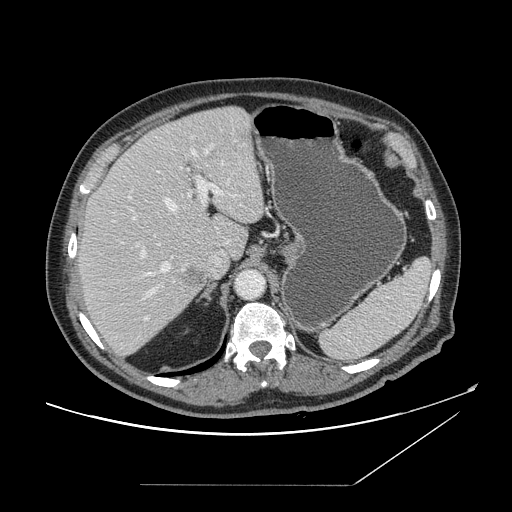
Contrast-enhanced abdominal CT, one axial slice. Position 110 of 166 along the scan axis. Intravenous contrast given. Soft-tissue window (W 400 / L 40 HU). 2.5 mm slice thickness. 512 × 512 image matrix. Male patient, age 80 years. Case-level facts recorded for this patient, not image findings: diagnosis: colorectal cancer liver metastases, imaged before liver resection; multiple liver metastases: no; largest metastasis: 2.2 cm; disease in both lobes: no.
Outlined on this slice (expert manual segmentation):
- hepatic veins: bounding box <133,150,196,298> (left, top, right, bottom; pixels)
- liver: <78,107,265,356>
- planned liver remnant (the part of the liver to remain after resection): <85,108,265,259>
- portal vein (with intrahepatic branches): <129,145,229,319>
- liver metastasis: <184,269,205,290>
- liver metastasis: <183,268,205,288>